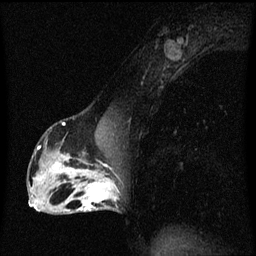
Breast MRI (dynamic contrast-enhanced), one sagittal slice; slice 32 of 60 in the series (ordered by position); dynamic contrast-enhanced series, image 2 of 3 at this slice position (ordered by acquisition); 1.5 T; TE 4.2 ms, TR 8.4 ms; 256 × 256 image matrix. Patient: female, 40 years.
Structures marked on this image (semi-automatically segmented with operator editing):
- analysis volume of interest (the breast-tissue region the enhancement analysis was run in; not a lesion): bounding box (x1, y1, x2, y2) in pixels: (76, 172, 119, 213)
- tumour enhancement mask (voxels above the 70 % enhancement threshold inside the analysis volume of interest): (76, 172, 118, 211)